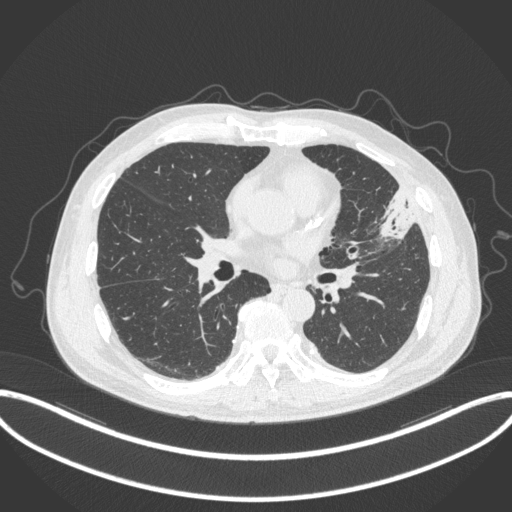
Chest CT, one axial slice. Slice 164 of 382 in the series (ordered by position). Reconstruction kernel B31f. 120 kVp. Lung window (W 1500 / L -600 HU). 1 mm slice thickness. 512 × 512 image matrix, field of view 415 × 415 mm. Patient: male, 64 years. Case-level facts recorded for this patient, not image findings: clinical TNM (as recorded): T4 N1 M0.
Outlined on this slice (rectangle marked by the reading radiologist):
- lung tumour (recorded histology: adenocarcinoma): bounding box [x1, y1, x2, y2] px = [375, 183, 417, 243]